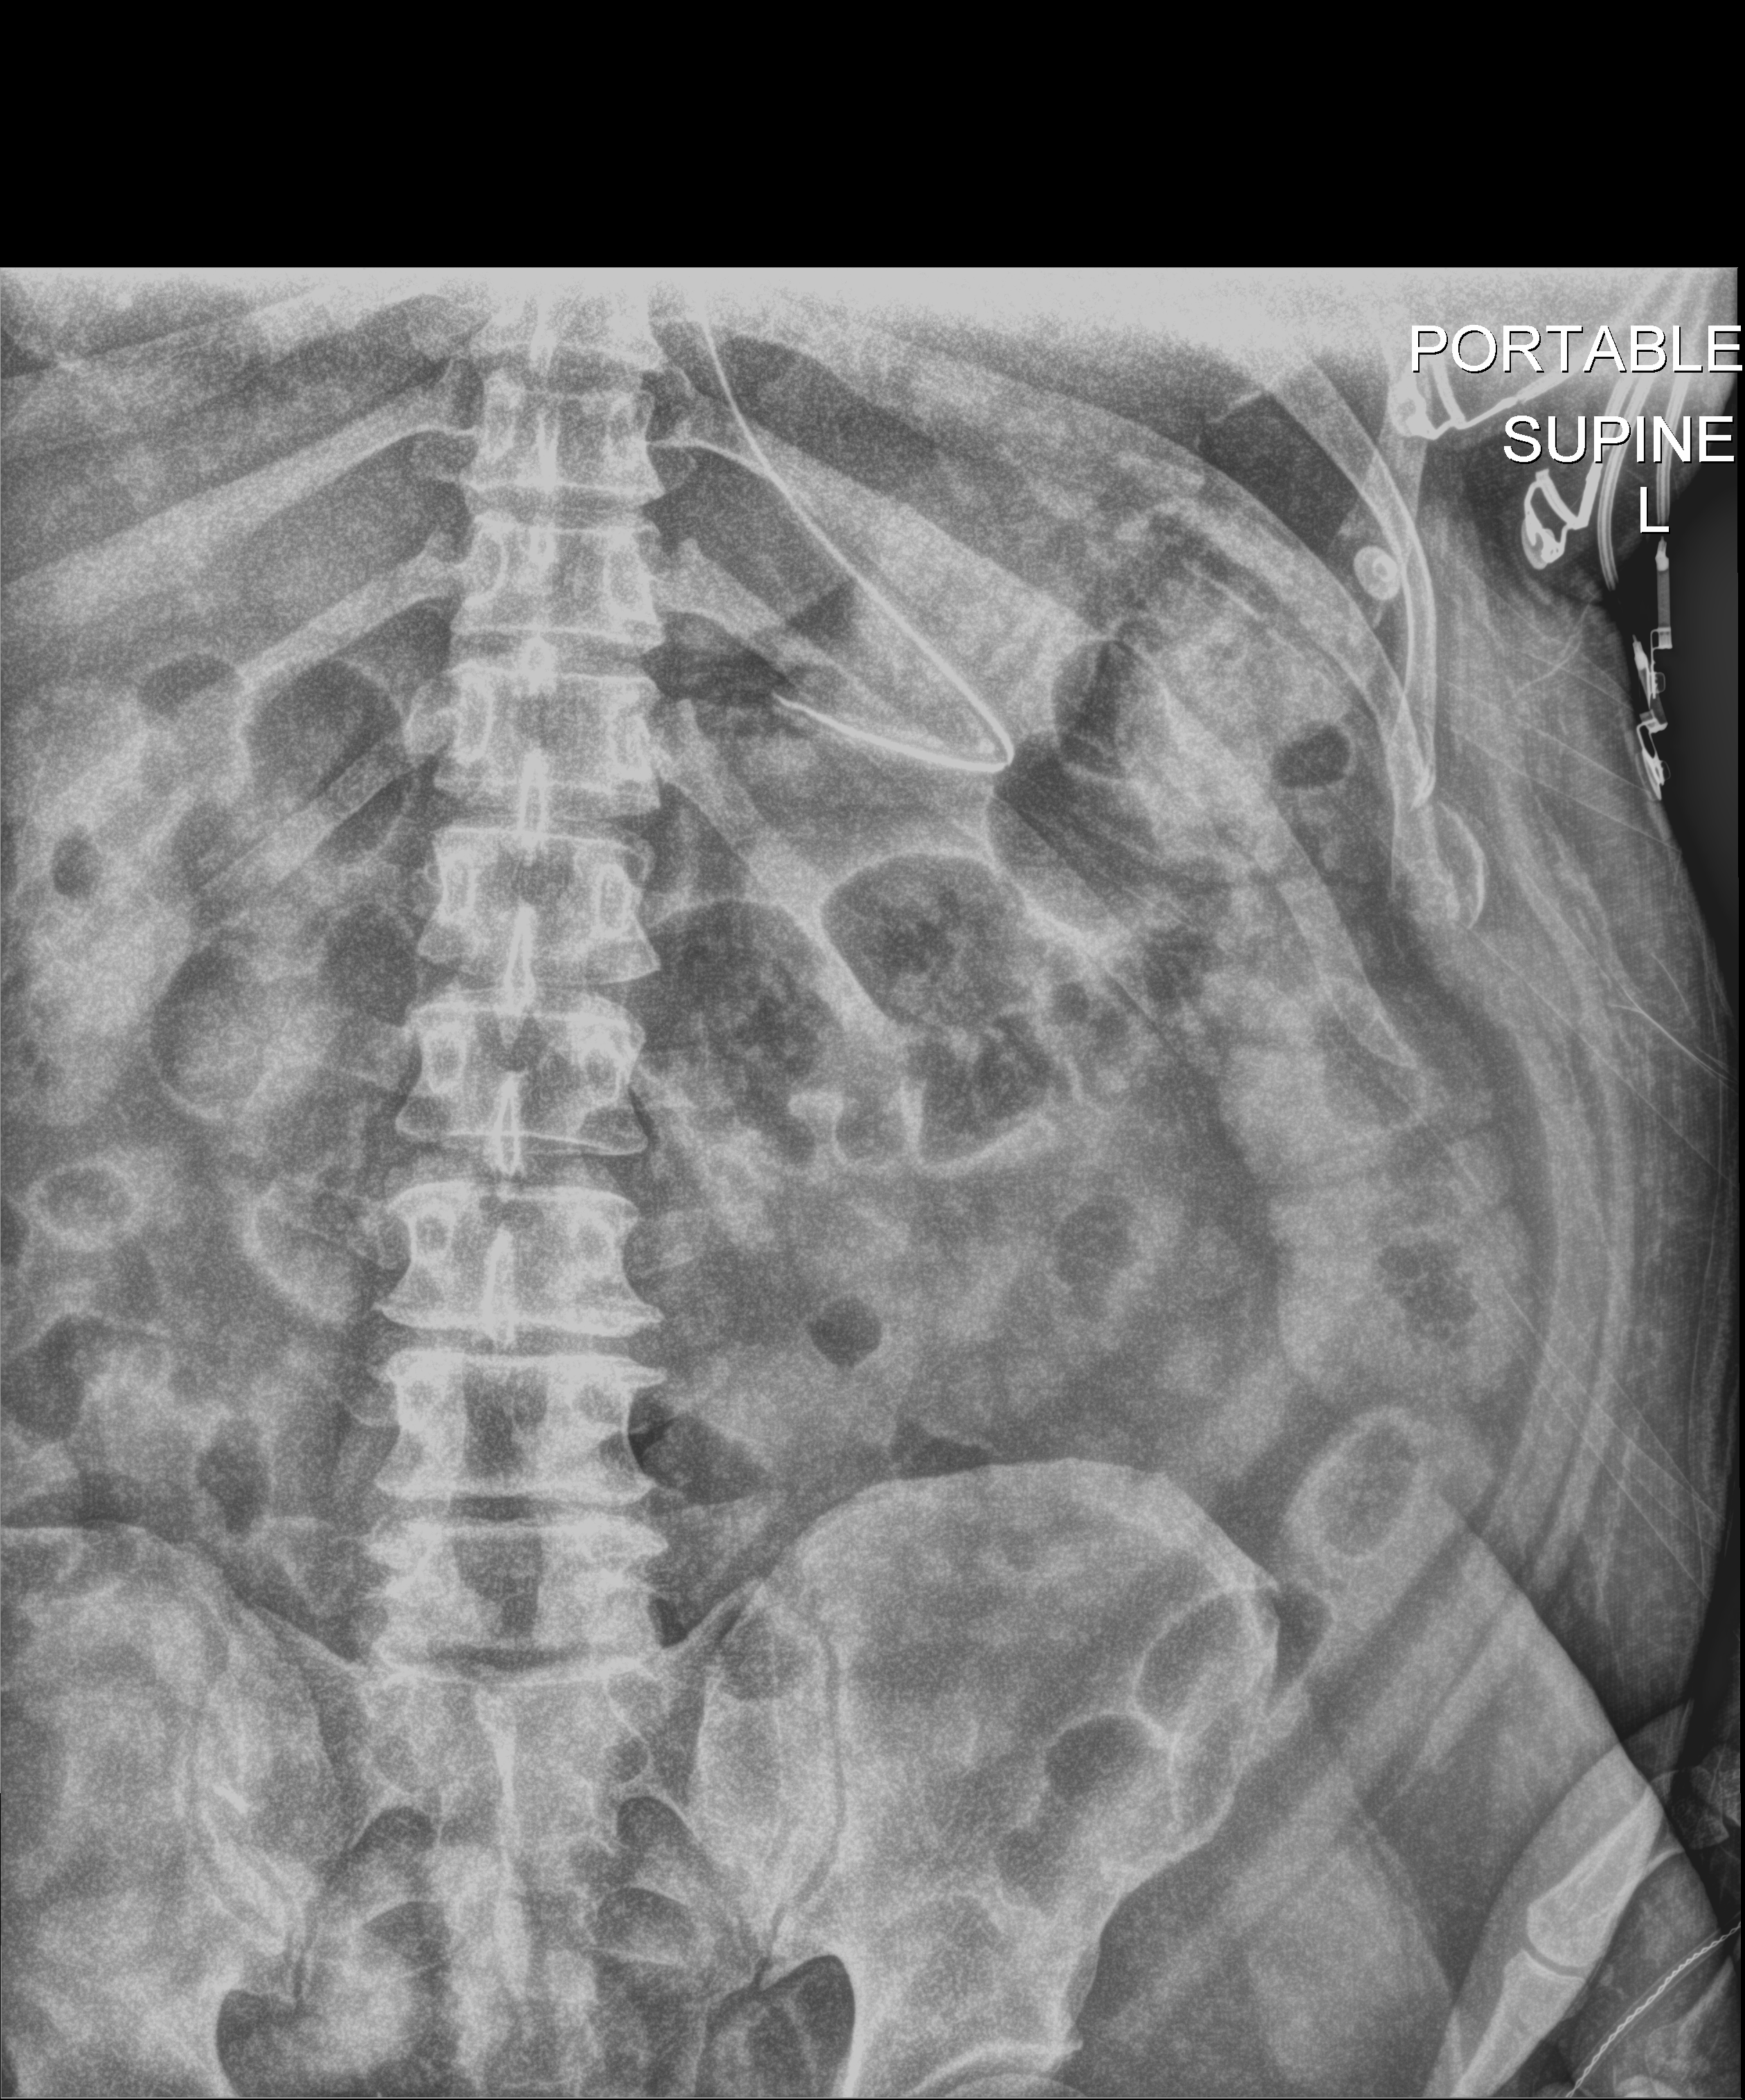
Bedside abdomen radiograph (digital radiography); anteroposterior (AP) projection. Male patient hospitalised with COVID-19, age 18–59 years.
From the hospital-stay record, not from the radiograph (when in the stay this image was taken is not recorded): admitted to intensive care during this hospital stay: yes; length of hospital stay: 96 days; COPD (admission record): no.